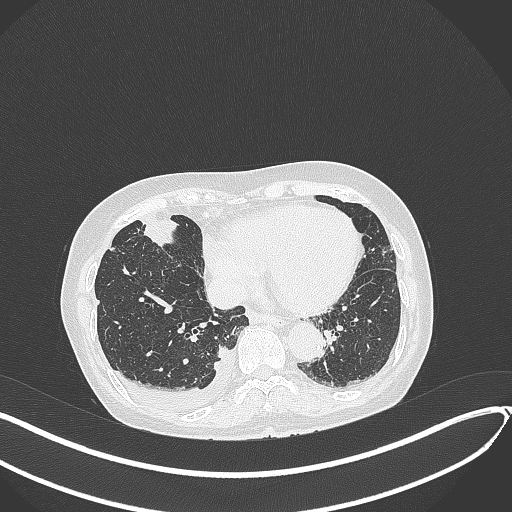
Chest CT, one axial slice. Position 118 of 418 along the scan axis. Reconstruction kernel B70f. Lung window (W 1500 / L -600 HU). 512 × 512 image matrix. Patient: female, 75 years. Case-level facts recorded for this patient, not image findings: clinical TNM (as recorded): T2a N3 M0.
Annotated regions visible in this slice (bounding box drawn by a radiologist):
- lung tumour (recorded histology: adenocarcinoma): bounding box <134,213,181,247> (left, top, right, bottom; pixels)